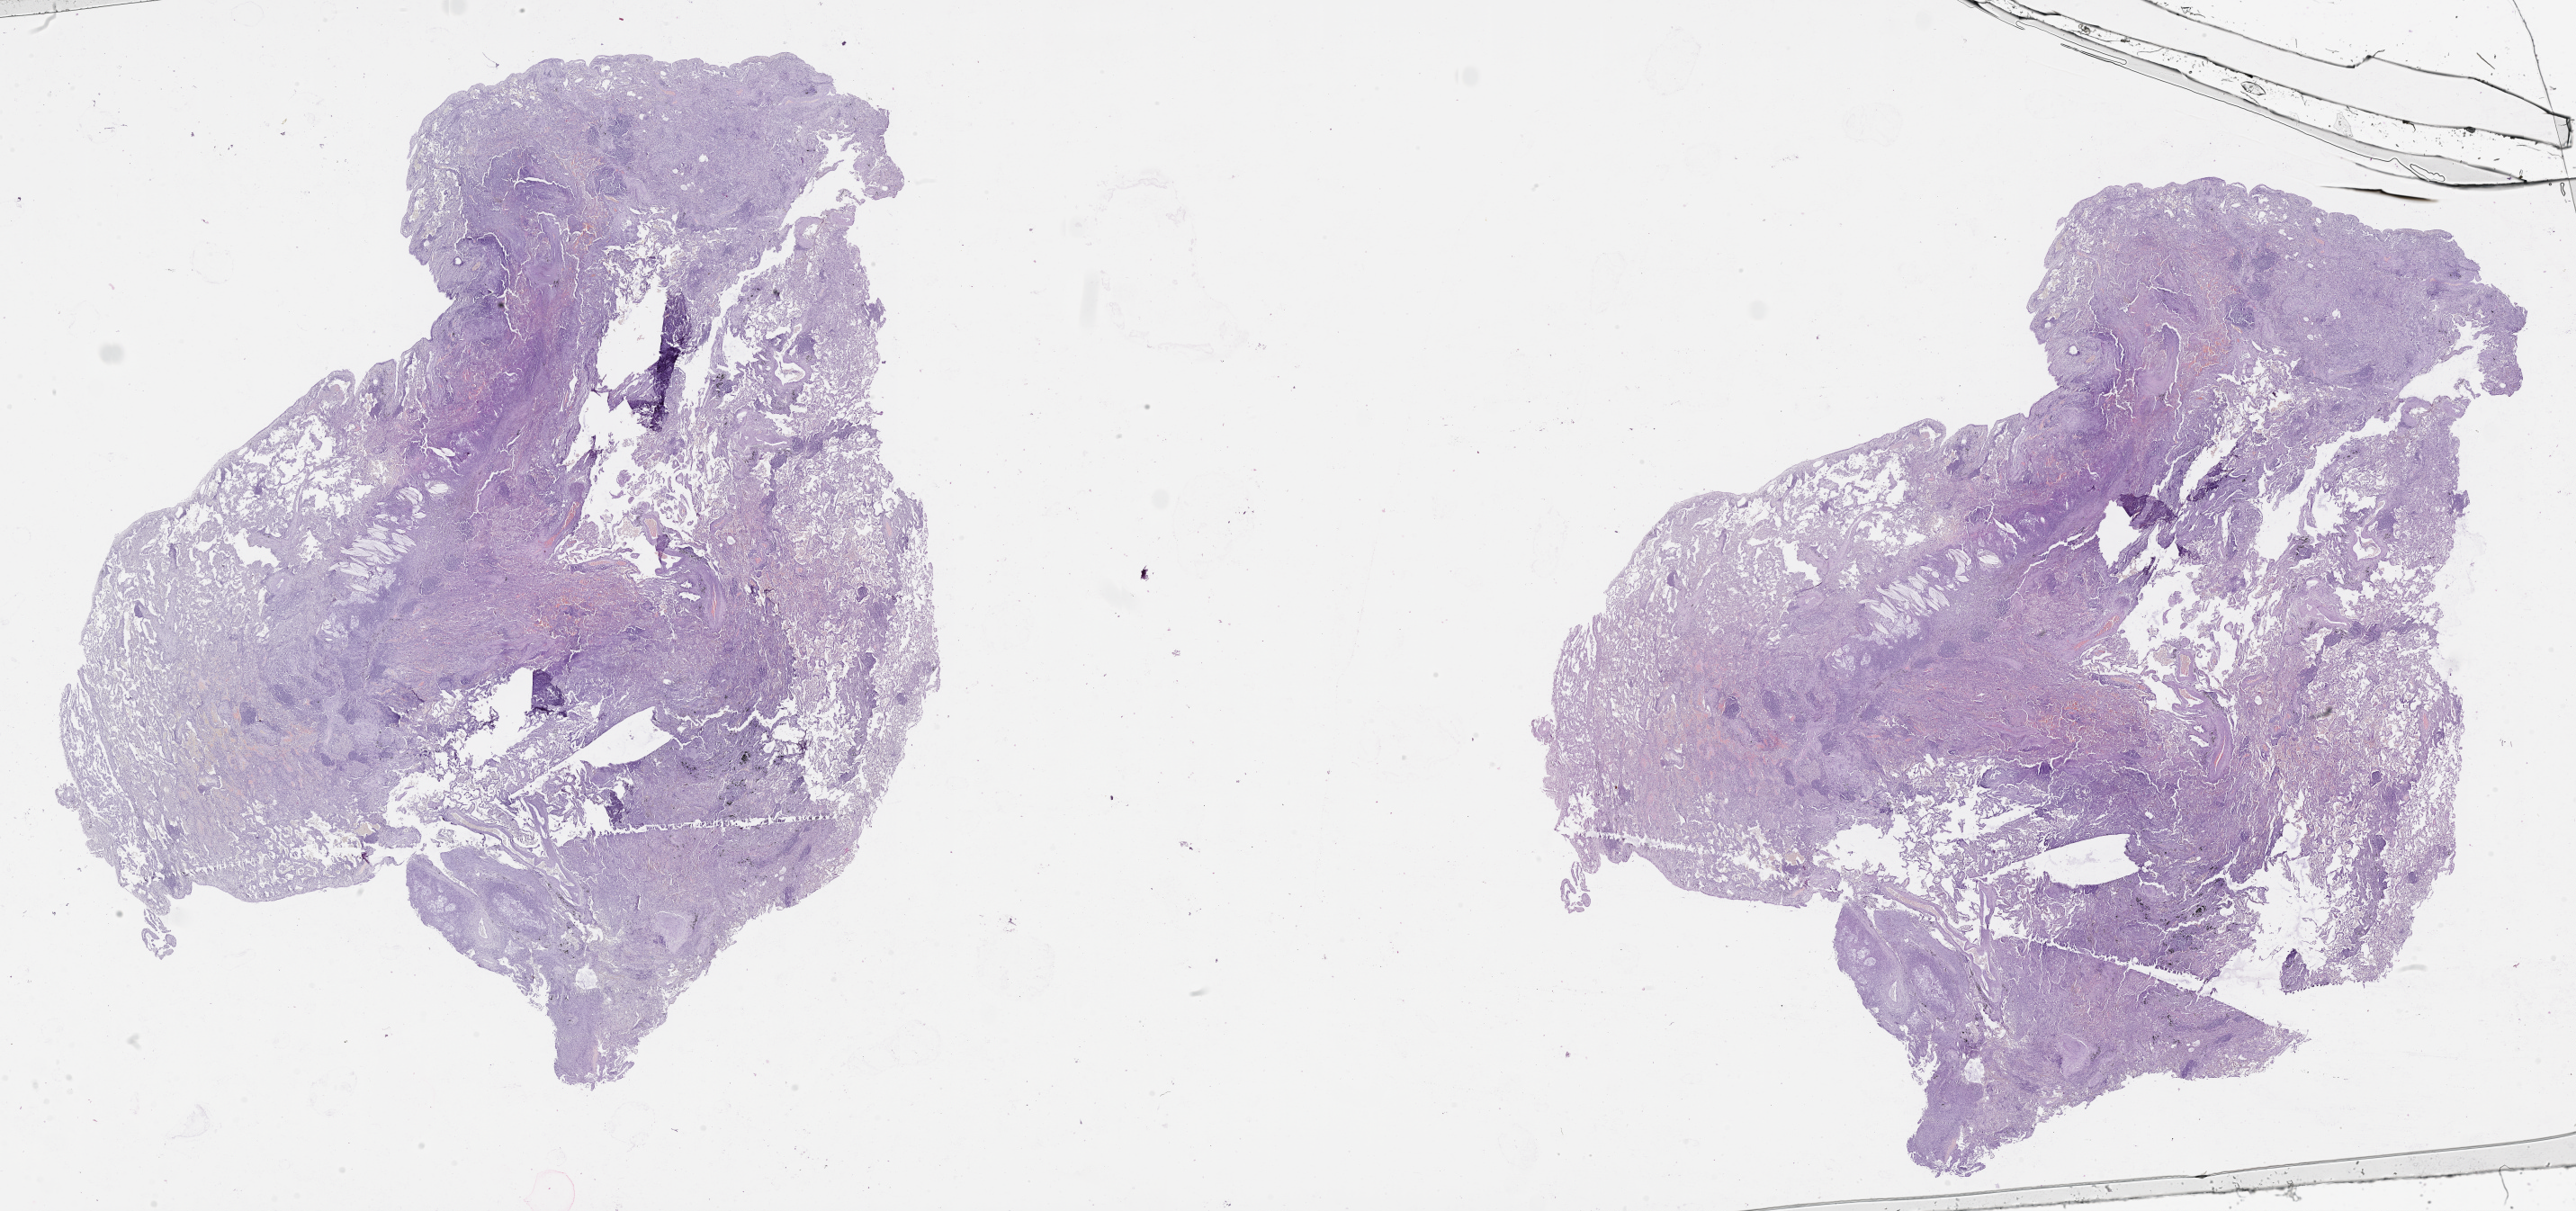
H&E whole-slide image — shown as a low-resolution overview of the whole scanned area (about 46.1 x 21.7 mm); tumour tissue sample, lung. 68-year-old male patient.
- patient diagnosis (cohort enrolment): squamous cell carcinoma (lung)